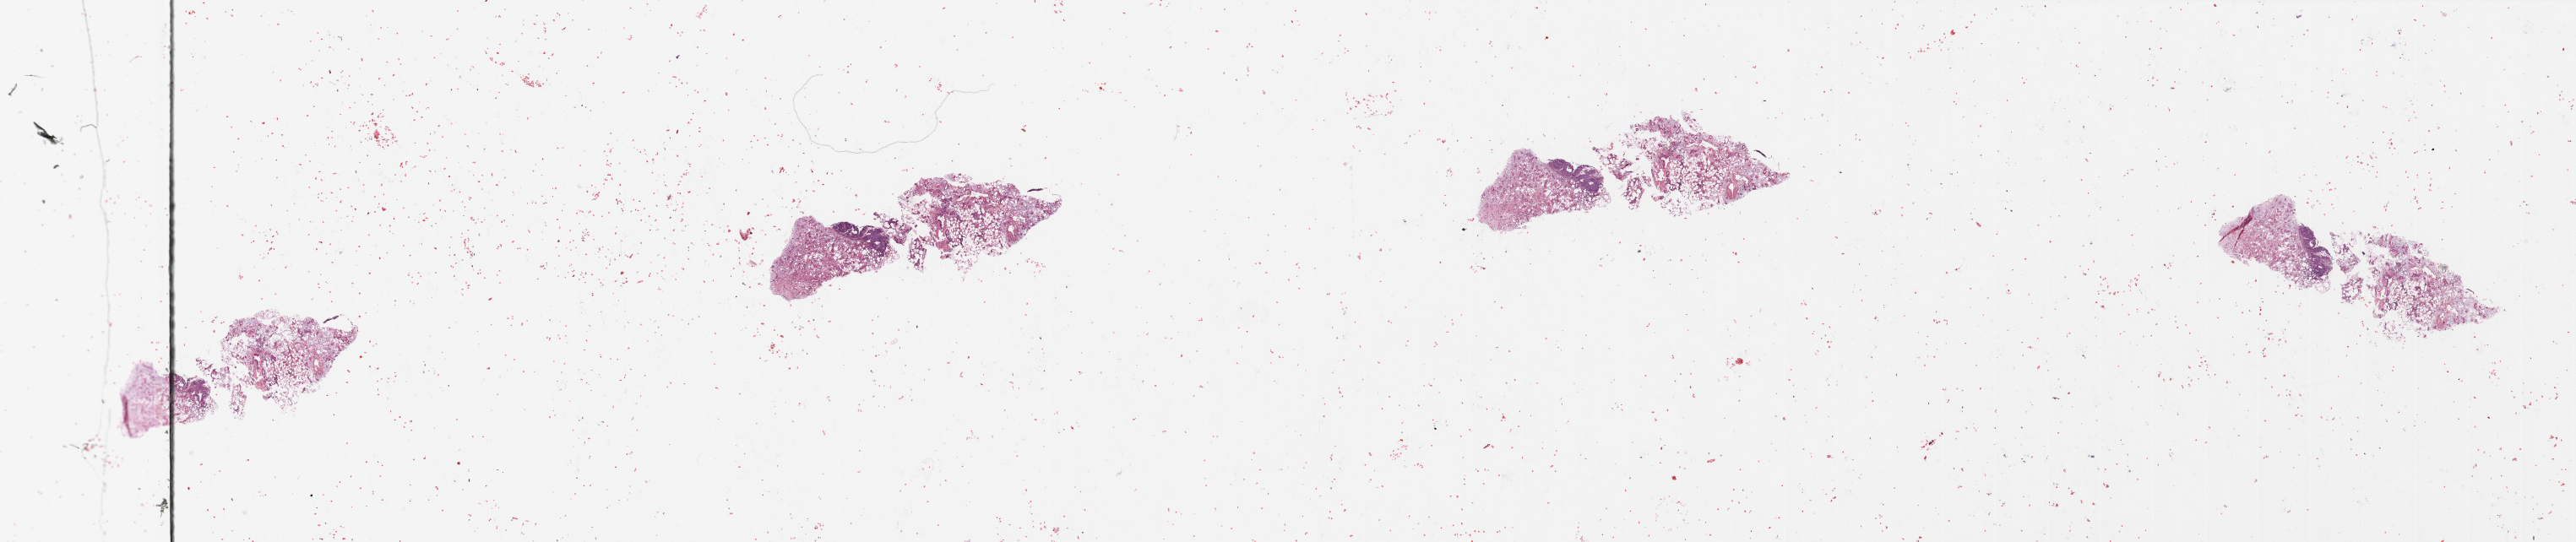
Whole-slide histology image, Hematoxylin and eosin (H&E) stained — low-resolution overview of the scanned area, about 48.2 x 10.2 mm. Tumour tissue sample, pancreas. Patient: female, age 63 years. Histologic grade: G2 (moderately differentiated).
Primary tumour site (as recorded): head. AJCC pathologic stage: IIB. Histologic diagnosis: Infiltrating duct carcinoma, NOS.